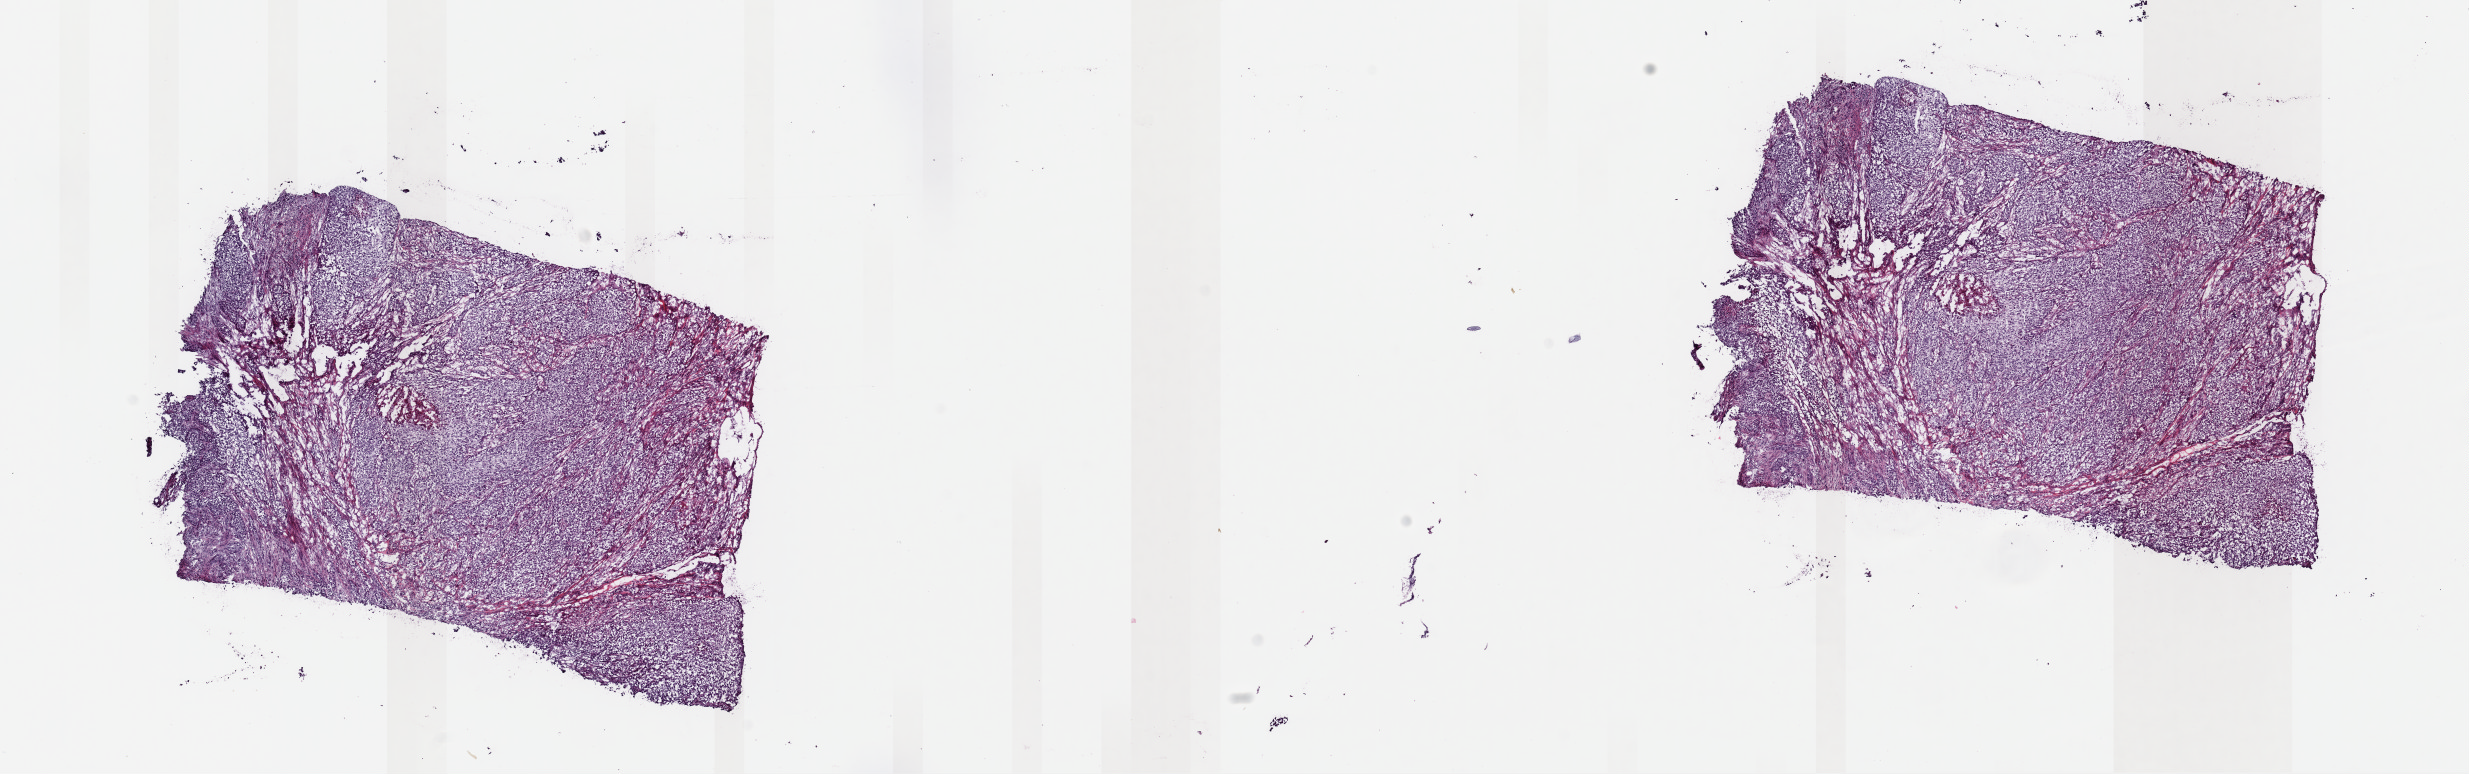
Whole-slide histology image, H&E, whole scanned area (about 19.5 x 6.1 mm, acquisition: 40x scan) shown as a low-resolution overview; frozen section from the top of the tissue portion; primary tumour sample from the cervix. Patient: female, age at initial diagnosis 25 years. Histologic grade: G2 (moderately differentiated). Pathologist review of this section (percent, as recorded): tumour cells 95%, tumour nuclei 90%, normal cells 0%, stromal cells 0%, necrosis 5%. Infiltration values recorded for this section: lymphocyte infiltration 1%, monocyte infiltration 1%, neutrophil infiltration 0%.
* lymph nodes positive (case pathology): 0 of 22 examined
* FIGO stage: IB
* pathologic diagnosis: Squamous cell carcinoma, keratinizing, NOS (cervix uteri)